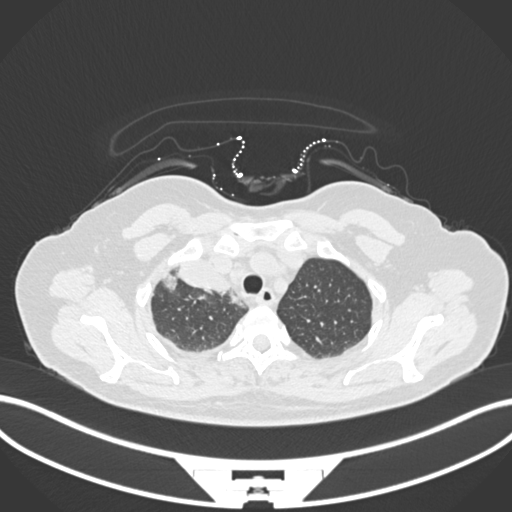
Chest CT, one axial slice. Reconstruction kernel B30f. 120 kVp. Lung window (W 1500 / L -600 HU). 512 × 512 image matrix. Patient: female, 52 years. From the clinical record (not read from this slice): clinical TNM (as recorded): T3 N1 M1.
Structures marked on this image (bounding box drawn by a radiologist):
- lung tumour (recorded histology: adenocarcinoma): bounding box (x1, y1, x2, y2) in pixels: (161, 261, 233, 299)